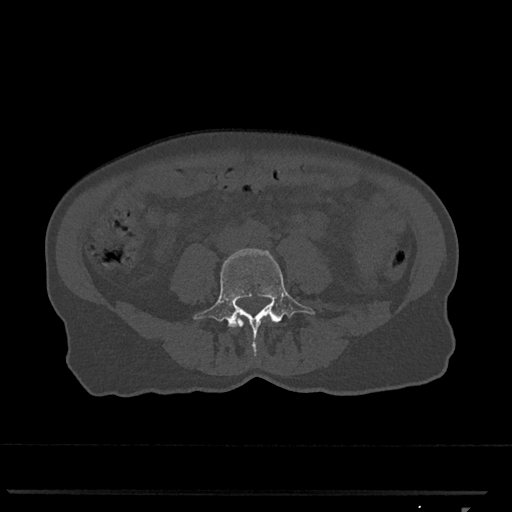
CT including the spine, one axial slice. Position 218 of 793 along the scan axis. 120 kVp. Bone window (W 1800 / L 400 HU). 512 × 512 image matrix, field of view 380 × 380 mm. Female patient, age 62 years. From the clinical record (not read from this slice): primary cancer: renal.
Structures marked on this image (semi-automatic segmentation, software-assisted and operator-edited):
- L3 vertebra: bounding box (x1, y1, x2, y2) in pixels: (236, 320, 243, 326)
- L4 vertebra: (193, 248, 315, 355)